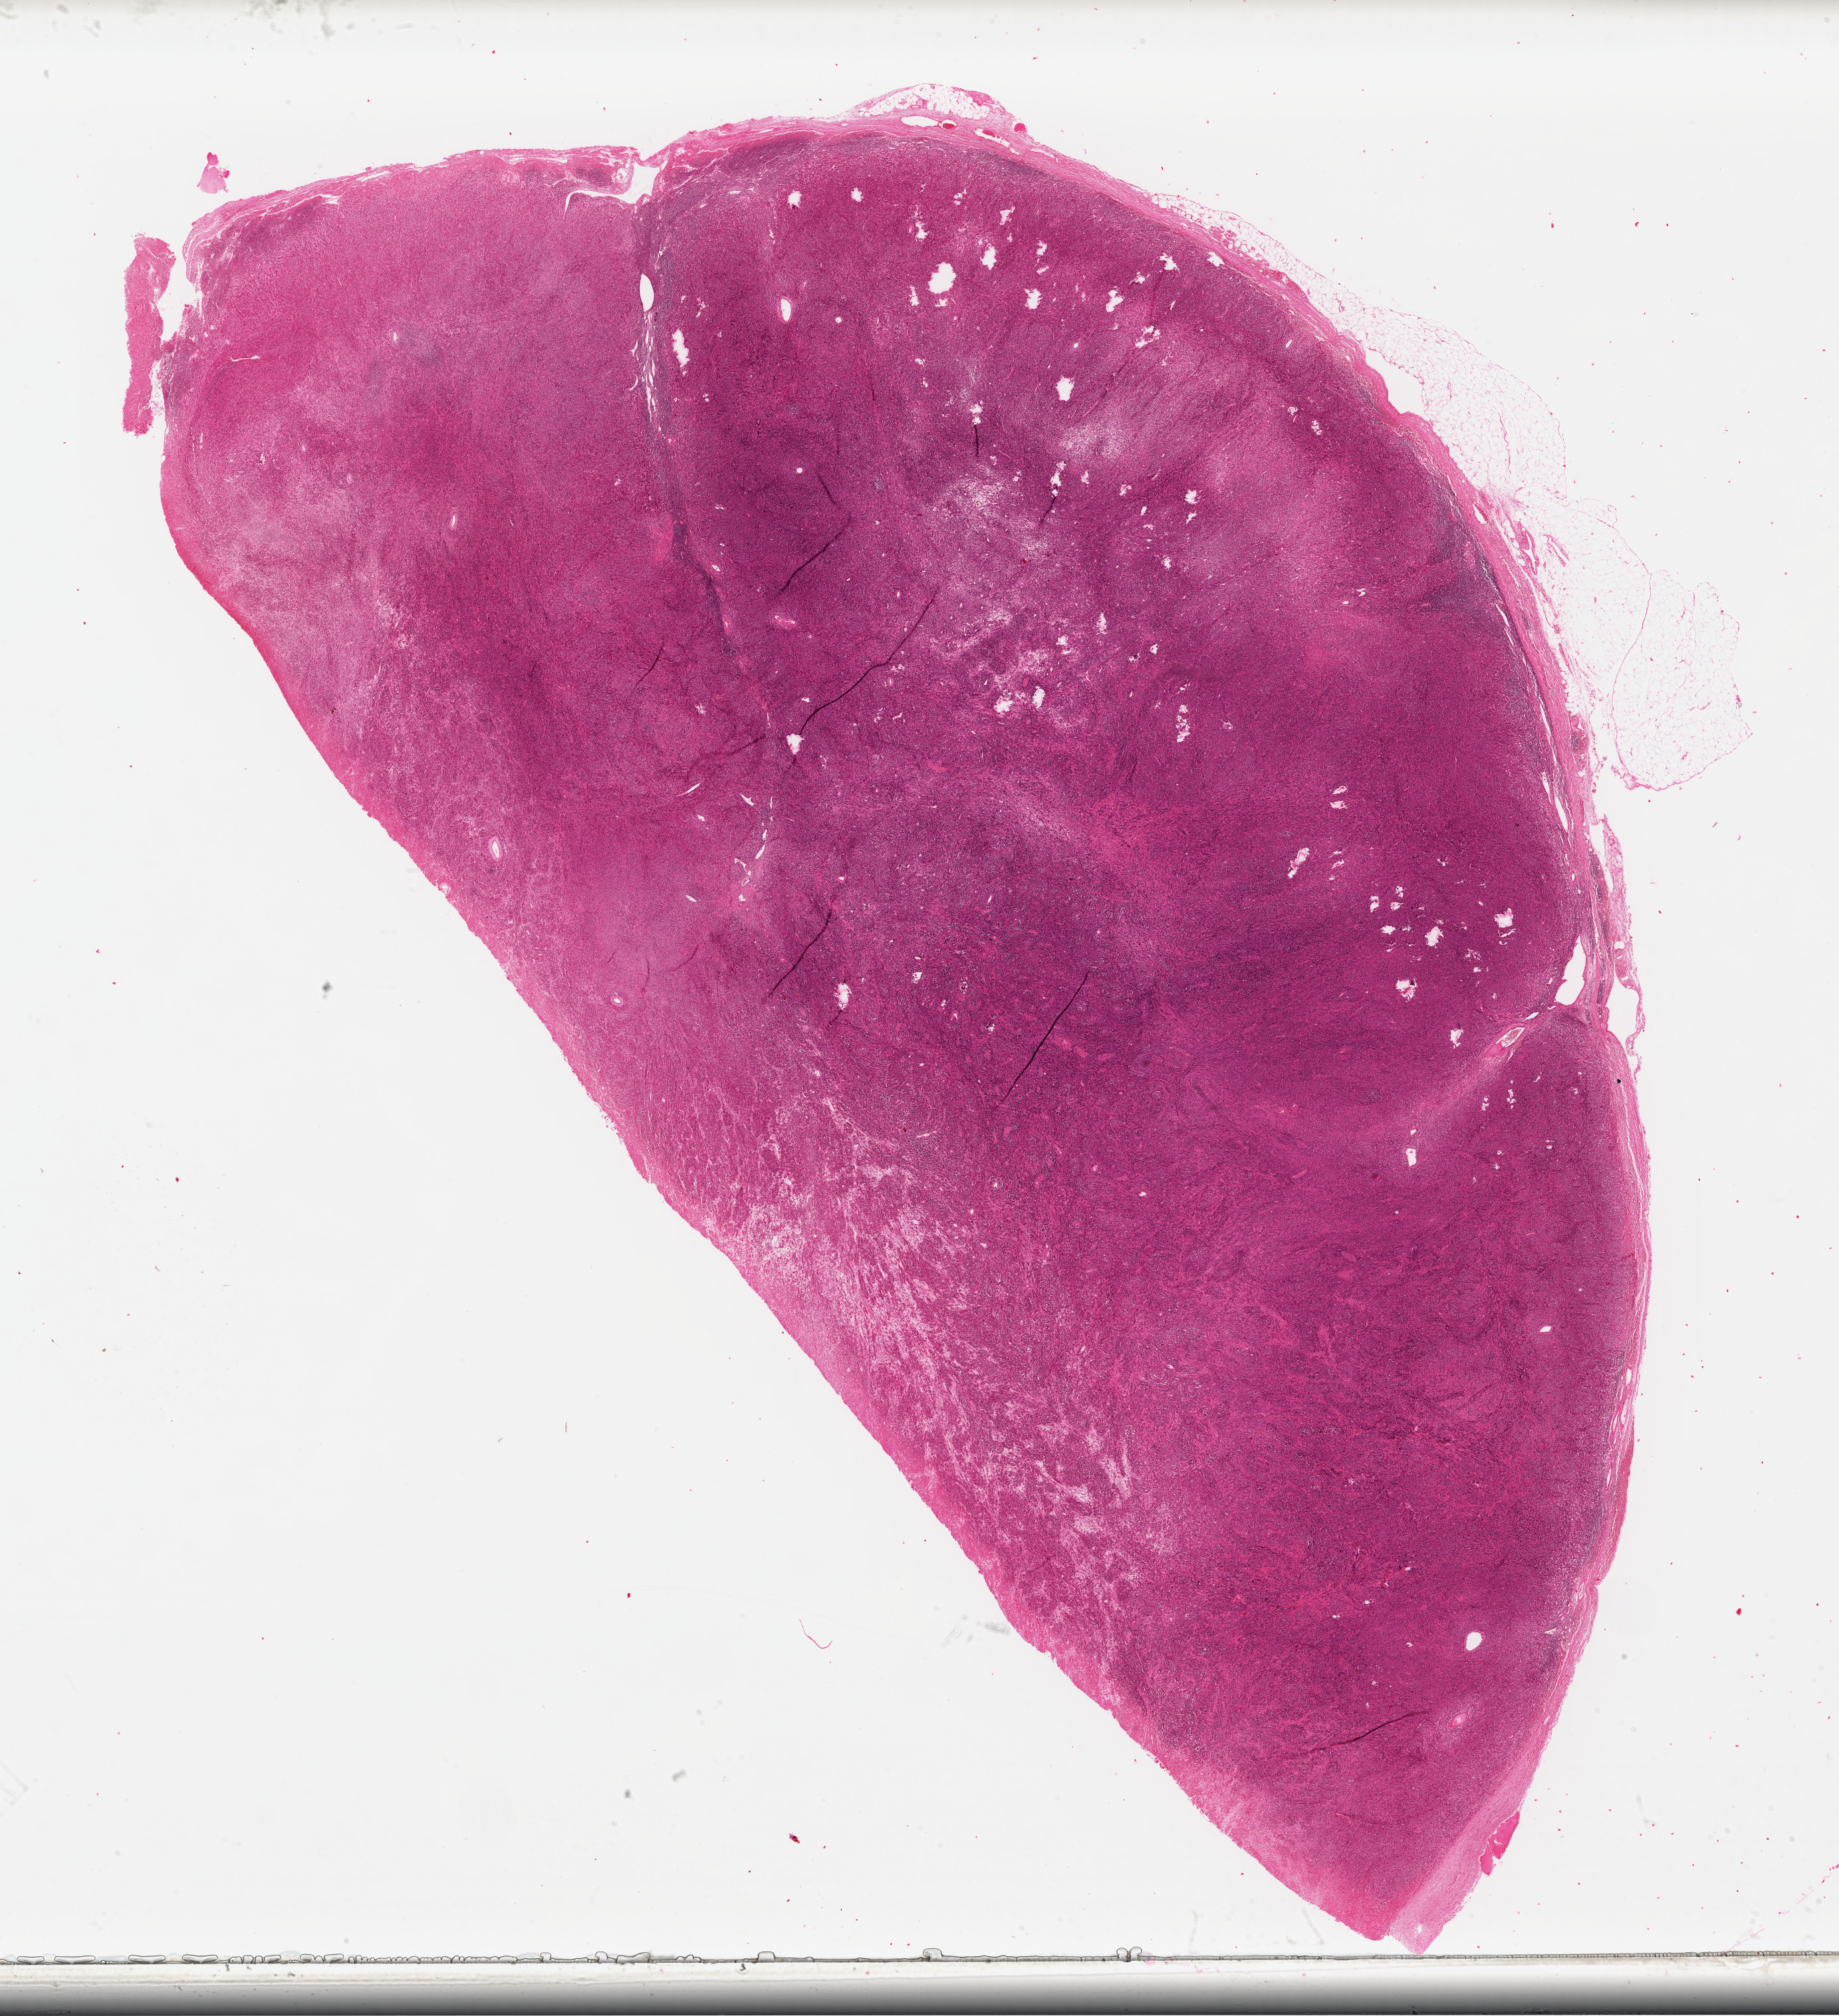
Whole-slide histology image, H&E-stained, low-resolution overview of the scanned area, about 21.7 x 23.8 mm (slide scanned at 40x); FFPE section; sample: primary tumour, skin. Female, age 63 years at initial diagnosis.
- pathologic diagnosis: Malignant melanoma, NOS